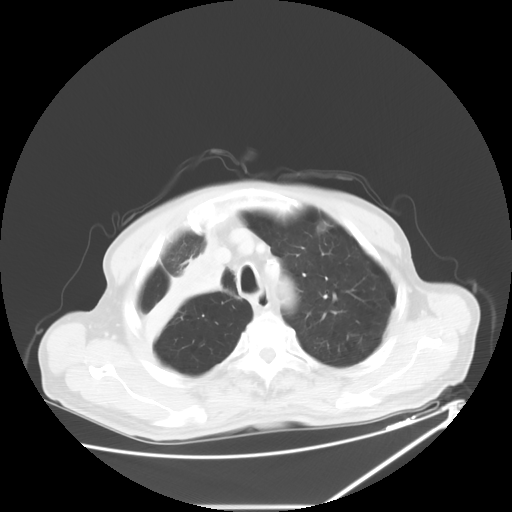
Chest CT, one axial slice; position 50 of 60 along the scan axis; lung window (W 1500 / L -600 HU); 512 × 512 image matrix, field of view 410 × 410 mm. Male patient, age 73 years. From the clinical record (not read from this slice): clinical TNM (as recorded): T2a N1 M0.
Annotated regions visible in this slice (rectangle marked by the reading radiologist):
- lung tumour (recorded histology: squamous cell carcinoma): bounding box (x1, y1, x2, y2) in pixels: (139, 230, 227, 343)